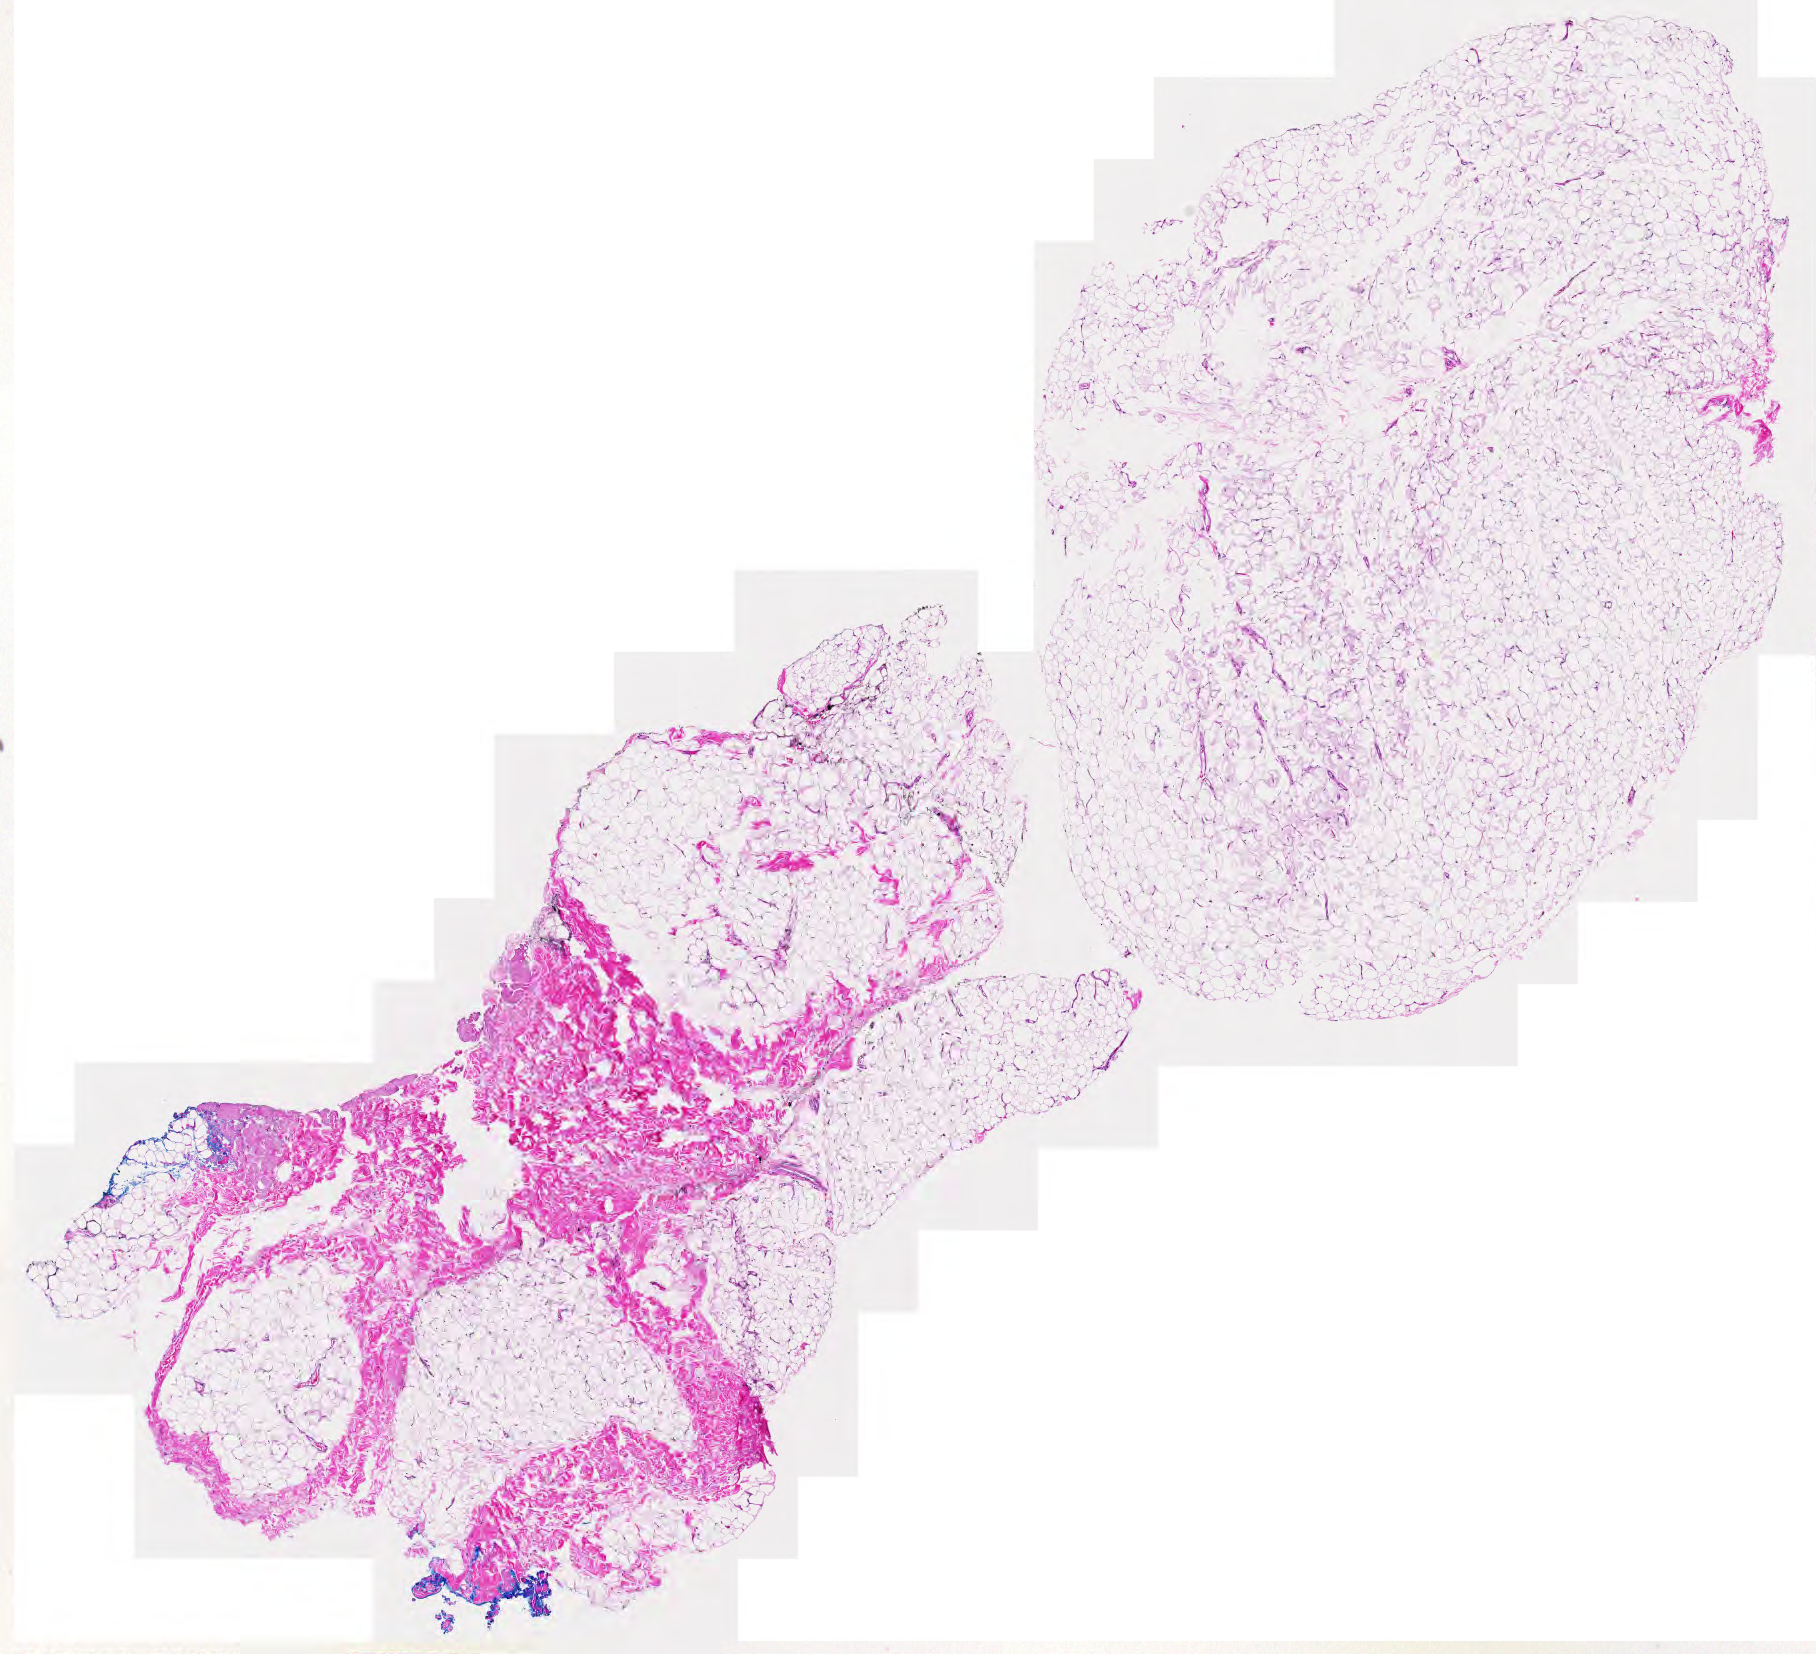
Digitized Hematoxylin and eosin (H&E) stained tissue section (whole slide), shown as a low-resolution overview of the whole scanned area (about 9.4 x 8.5 mm, slide scanned at 20x). Normal (non-tumour) tissue sample. 41-year-old female patient.
- this section: normal (non-tumour) tissue from the same patient
- patient diagnosis (cohort enrolment): sarcoma (site not recorded at cohort level)